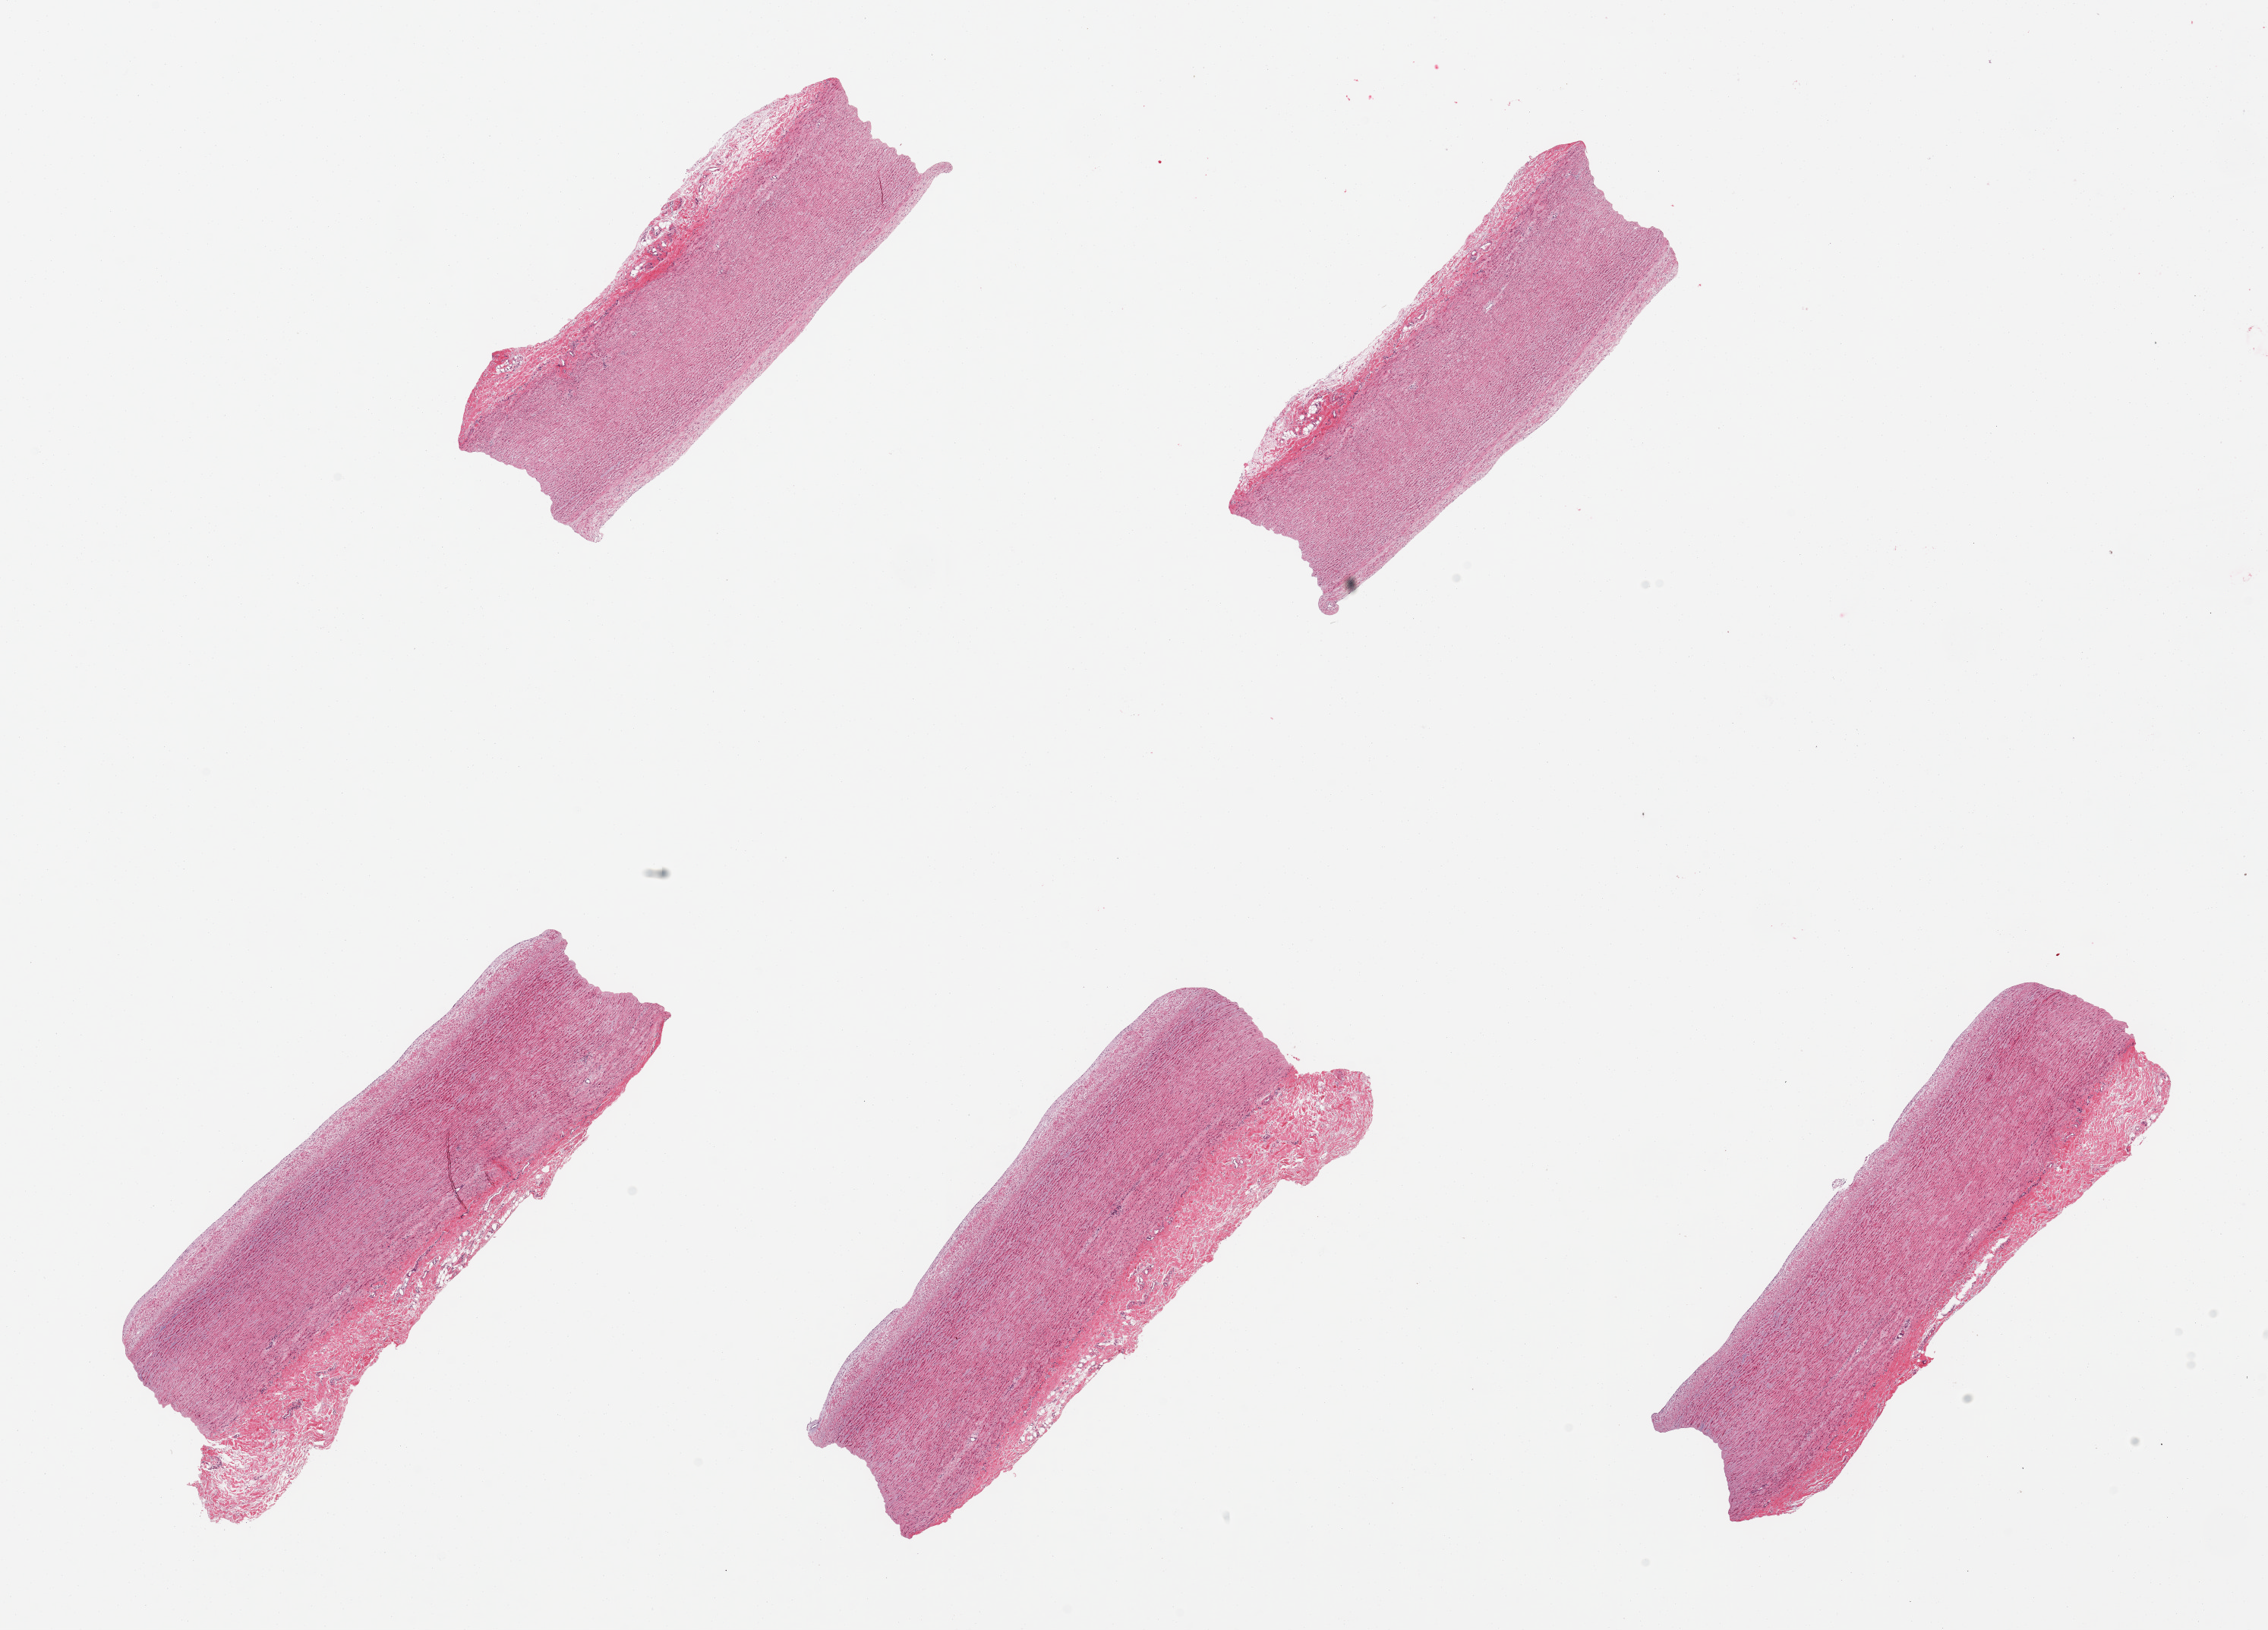
Hematoxylin and eosin (H&E) whole-slide image, brightfield — low-resolution overview of the scanned area, about 23.6 x 17.0 mm (slide scanned at 20x). PAXgene-fixed, paraffin-embedded tissue. Sampled site (target tissue): aorta. Tissue donor sample. Donor: female.
Review note (as recorded): 5 pieces; atherosis.